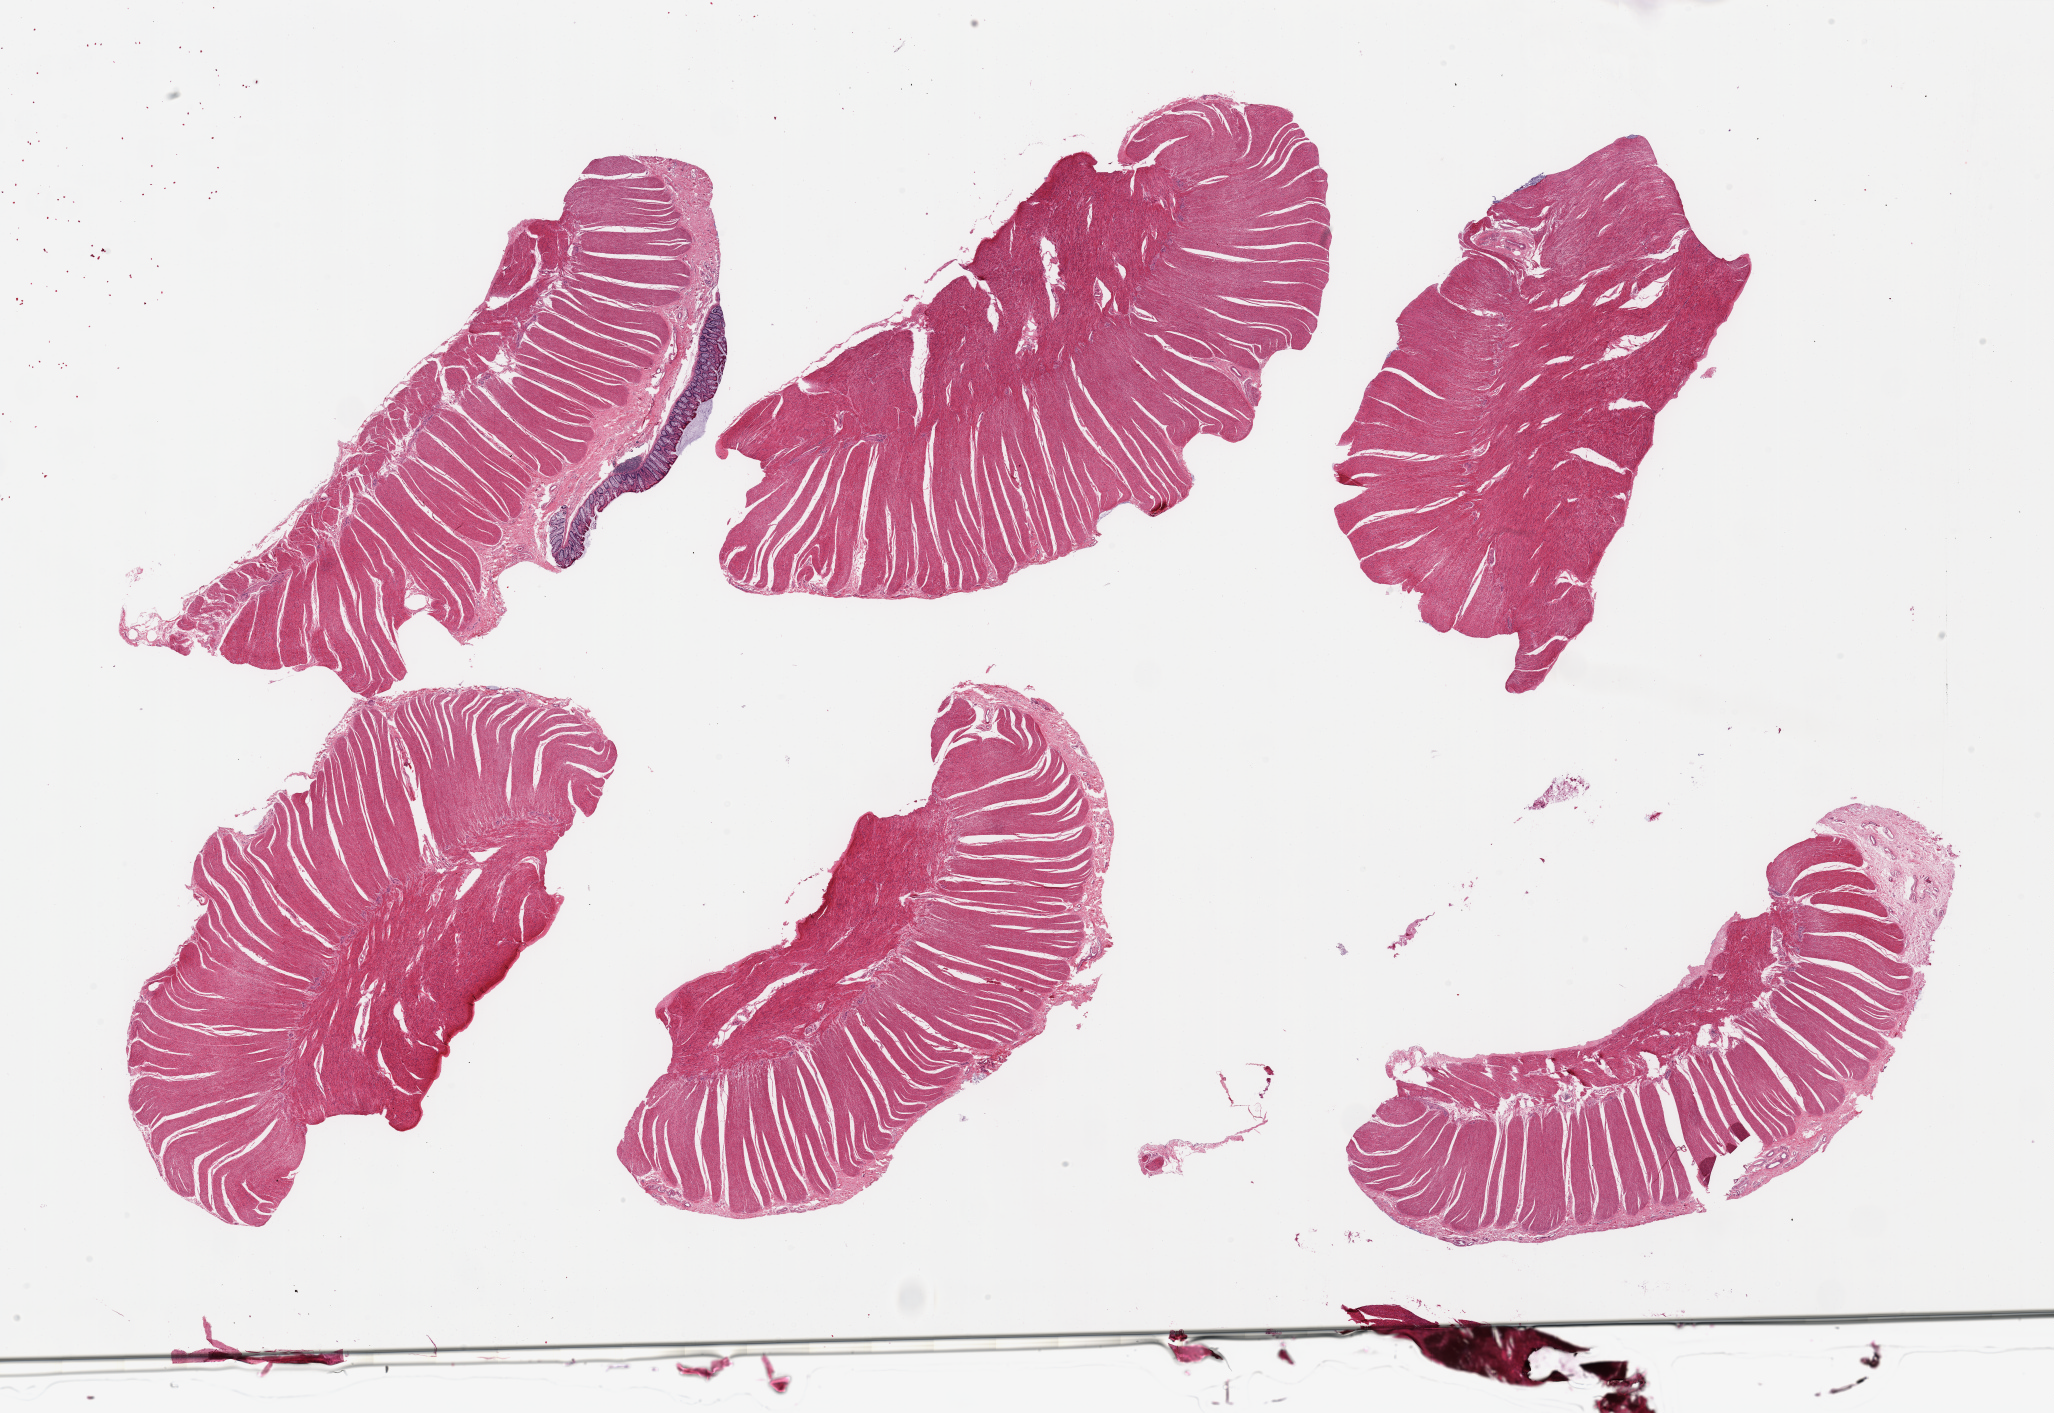
Whole-slide image, haematoxylin and eosin stain, brightfield, shown as a low-resolution overview of the whole scanned area (about 32.5 x 22.3 mm, from a 20x scan); PAXgene-fixed, paraffin-embedded tissue; section of sigmoid colon (target tissue); tissue donor sample. Donor sex: male.
Pathologist's review note for this sample: 6 pieces; well dissected except for 1 piece with 4mm mucosa.